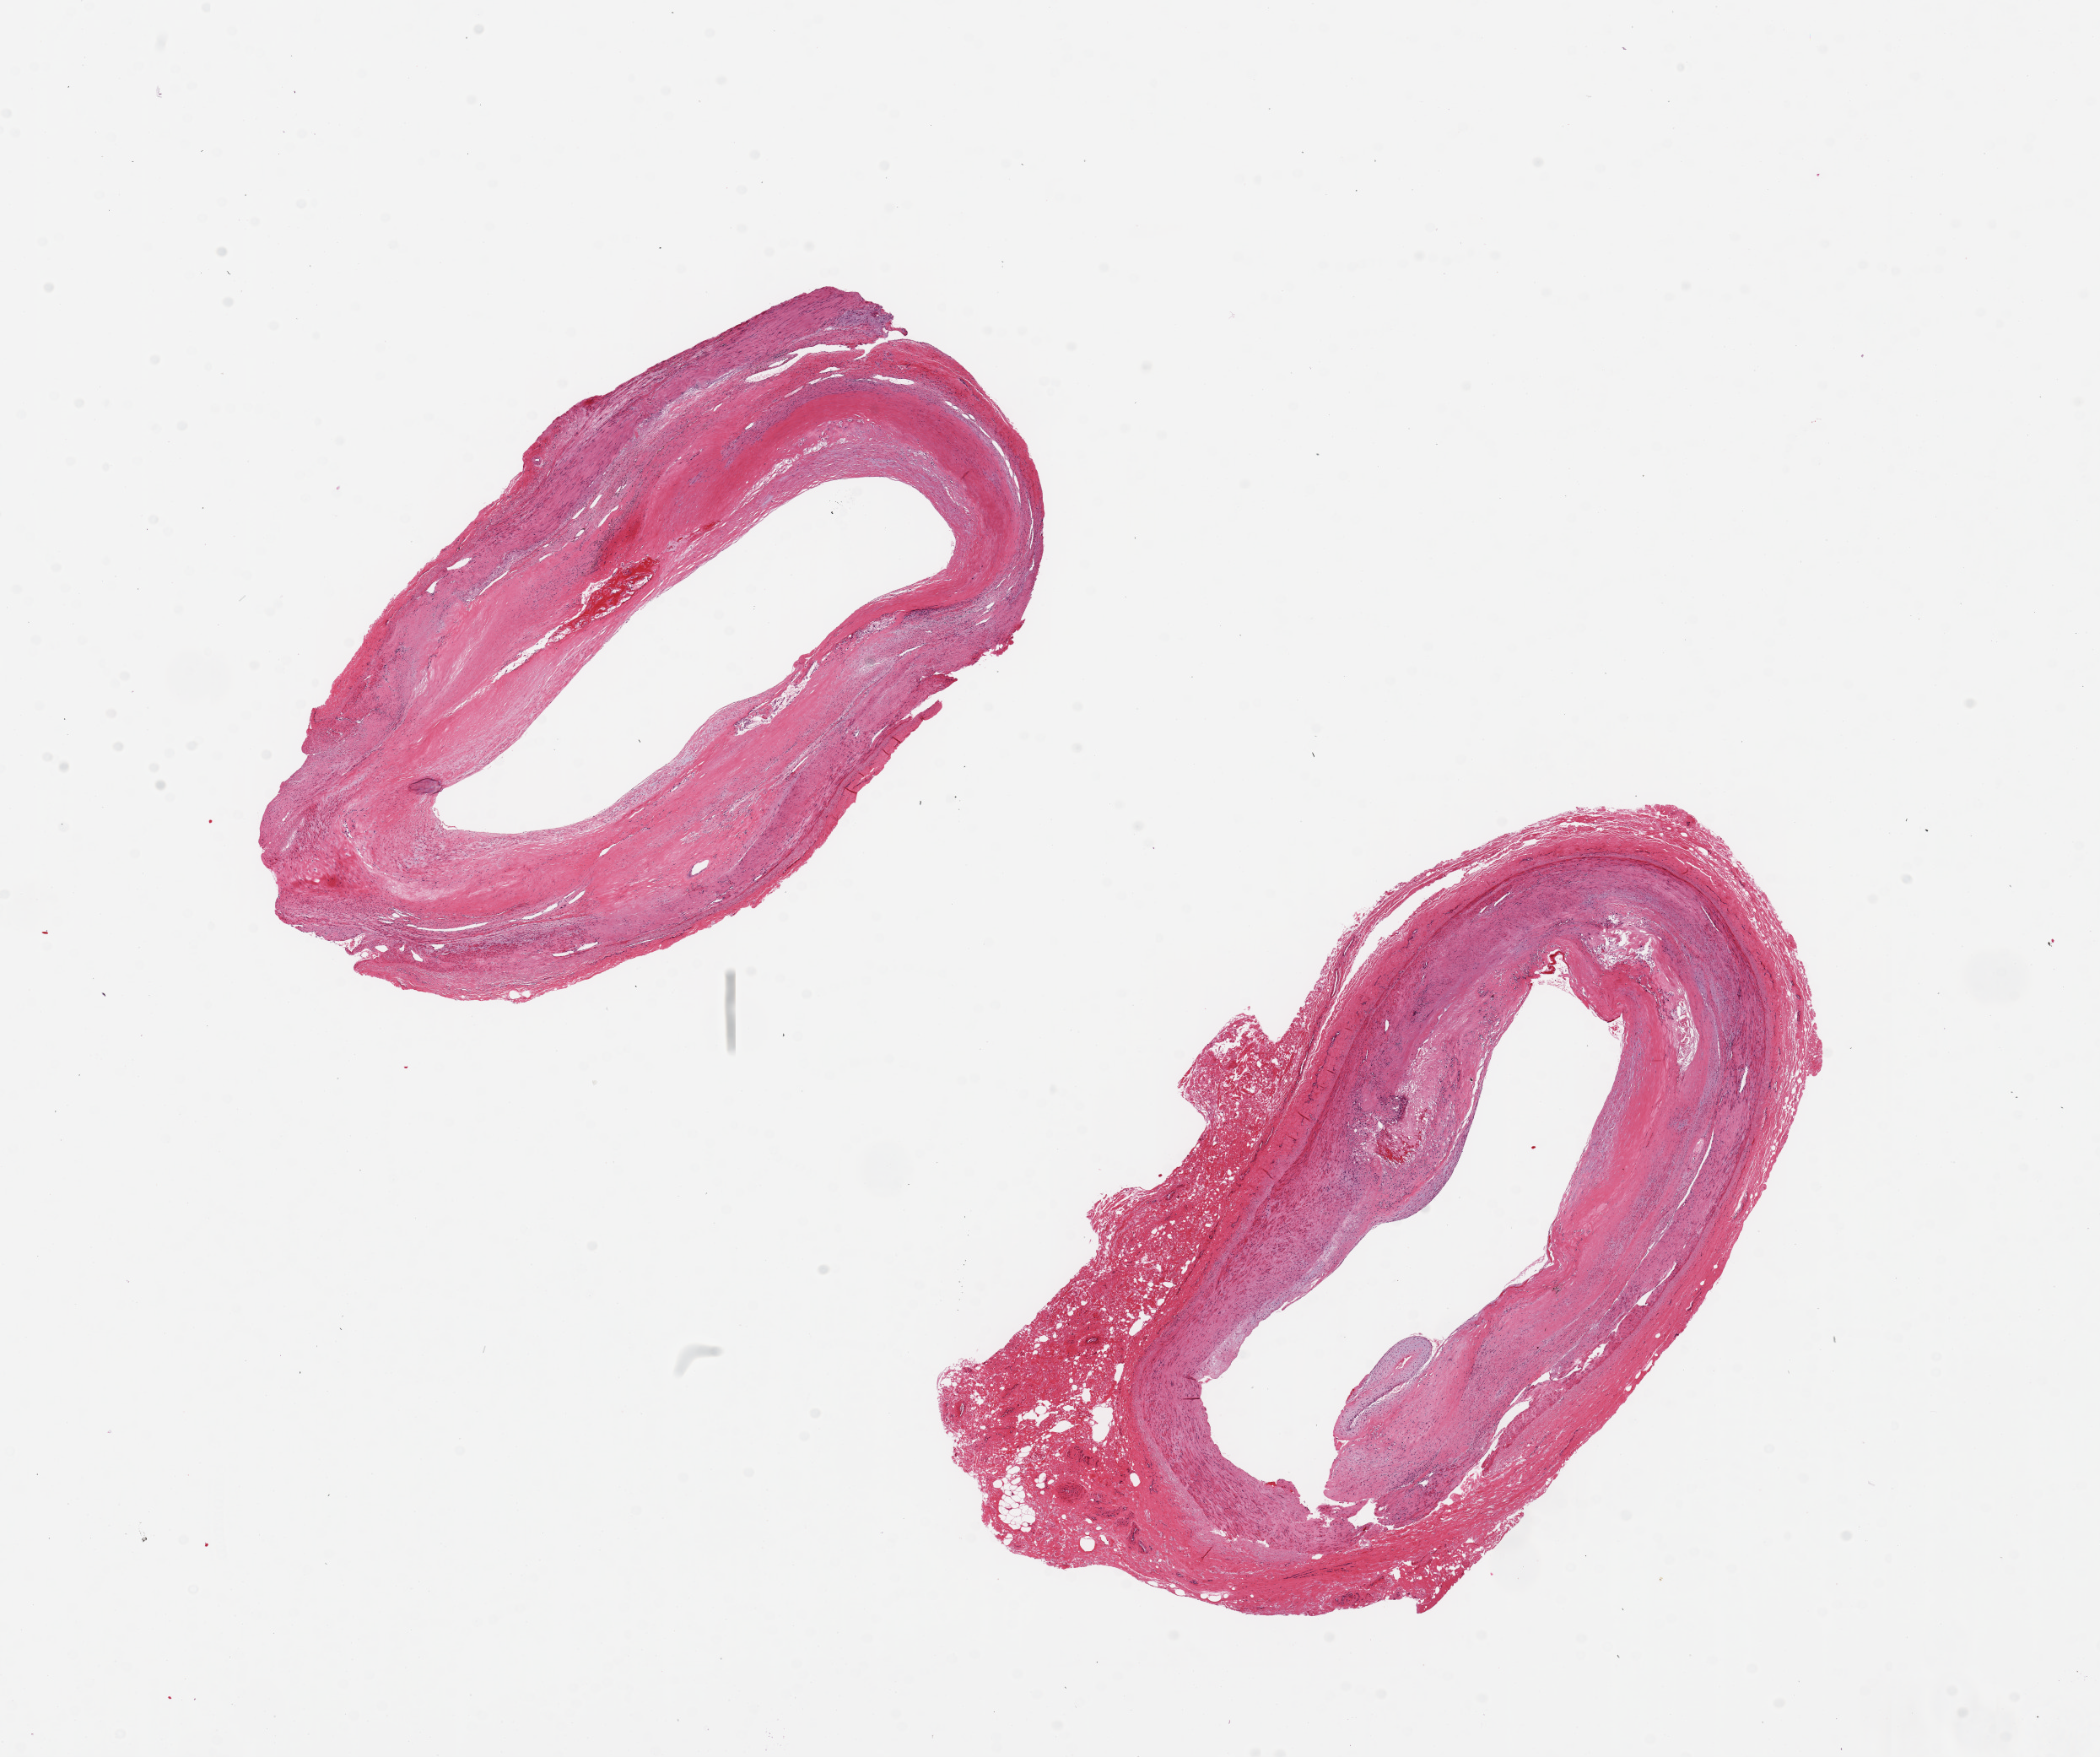
Hematoxylin and eosin (H&E) whole-slide image — a low-resolution overview of the entire scanned area, about 19.7 x 16.5 mm, PAXgene-fixed paraffin-embedded (PFPE) section, sampled site (target tissue): tibial artery, tissue donor sample. Donor sex: male.
Pathologist's review note for this sample: 2 pieces ~5mm d., moderate atherosclerosis, evidence of dissection.